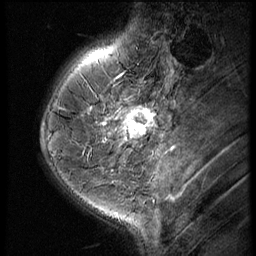
Breast MRI (dynamic contrast-enhanced), one sagittal slice; position 19 of 60 along the scan axis; 3 images stored at this slice position (order not interpretable as contrast timing); 1.5 T; TE 4.2 ms, TR 9 ms; 256 × 256 image matrix, field of view 180 × 180 mm. Female patient, age 38 years. Case-level facts recorded for this patient, not image findings: setting: breast cancer imaged before/during neoadjuvant chemotherapy; receptor status: triple-negative.
Outlined on this slice (semi-automatic segmentation, software-assisted and operator-edited):
- analysis volume of interest (the breast-tissue region the enhancement analysis was run in; not a lesion): box from (x=119, y=93) to (x=165, y=150) px
- tumour enhancement mask (voxels above the 140 % enhancement threshold inside the analysis volume of interest): (x=119, y=107)–(x=156, y=141)